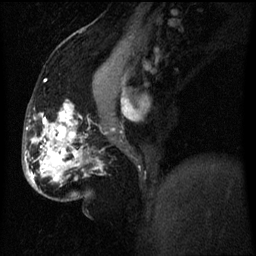
Breast MRI (dynamic contrast-enhanced), one sagittal slice. Slice 30 of 60 in the series (ordered by position). Dynamic contrast-enhanced series, image 2 of 3 at this slice position (ordered by acquisition). 1.5 T. TE 4.2 ms, TR 8 ms. 2.5 mm slice thickness. 256 × 256 image matrix. Patient: female, 50 years.
Outlined on this slice (semi-automatic segmentation, software-assisted and operator-edited):
- analysis volume of interest (the breast-tissue region the enhancement analysis was run in; not a lesion): box from (x=32, y=128) to (x=75, y=183) px
- tumour enhancement mask (voxels above the 70 % enhancement threshold inside the analysis volume of interest): (x=42, y=152)–(x=61, y=167)